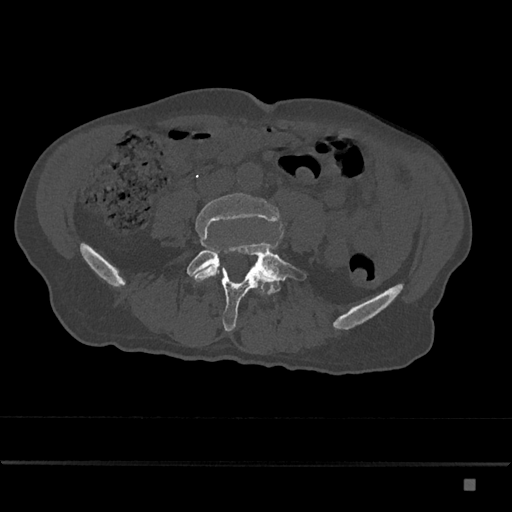
CT including the spine, one axial slice; slice 300 of 797 in the series (ordered by position); 120 kVp; bone window (W 1800 / L 400 HU); 512 × 512 image matrix. Male patient, age 72 years. From the clinical record (not read from this slice): primary cancer: prostate.
Outlined on this slice (semi-automatic segmentation, software-assisted and operator-edited):
- L4 vertebra: bounding box [x1, y1, x2, y2] px = [191, 193, 282, 282]
- L5 vertebra: [187, 242, 307, 332]